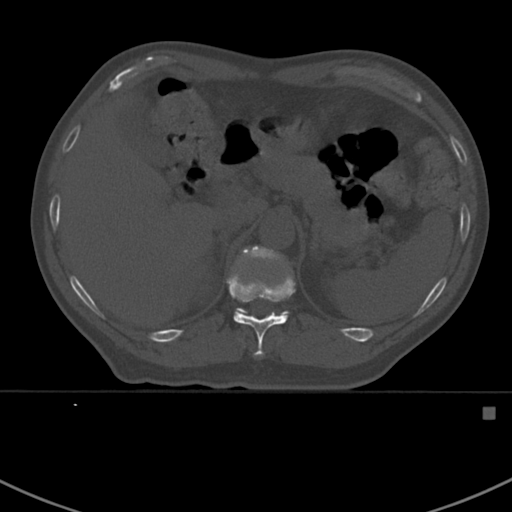
CT including the spine, one axial slice. Position 344 of 412 along the scan axis. Reconstruction kernel Br40s. 120 kVp. Bone window (W 1800 / L 400 HU). 1.5 mm slice thickness. 512 × 512 image matrix, field of view 358 × 358 mm. Male patient, age 59 years. From the clinical record (not read from this slice): primary cancer: prostate.
Annotated regions visible in this slice (semi-automatically segmented with operator editing):
- T11 vertebra: box from (x=227, y=264) to (x=295, y=358) px
- T12 vertebra: (x=235, y=245)–(x=289, y=314)